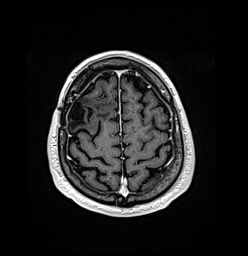
Brain MRI from a brain-tumour surgery series, one axial slice. Slice 34 of 176 in the series (ordered by position). T1-weighted post-contrast. 248 × 256 image matrix, field of view 242 × 250 mm. From the clinical record (not read from this slice): histopathology: Oligodendroglioma; WHO grade: 3; IDH mutation: yes.
Structures marked on this image (outlined manually by an expert reader):
- previous resection cavity: box from (x=70, y=99) to (x=86, y=124) px